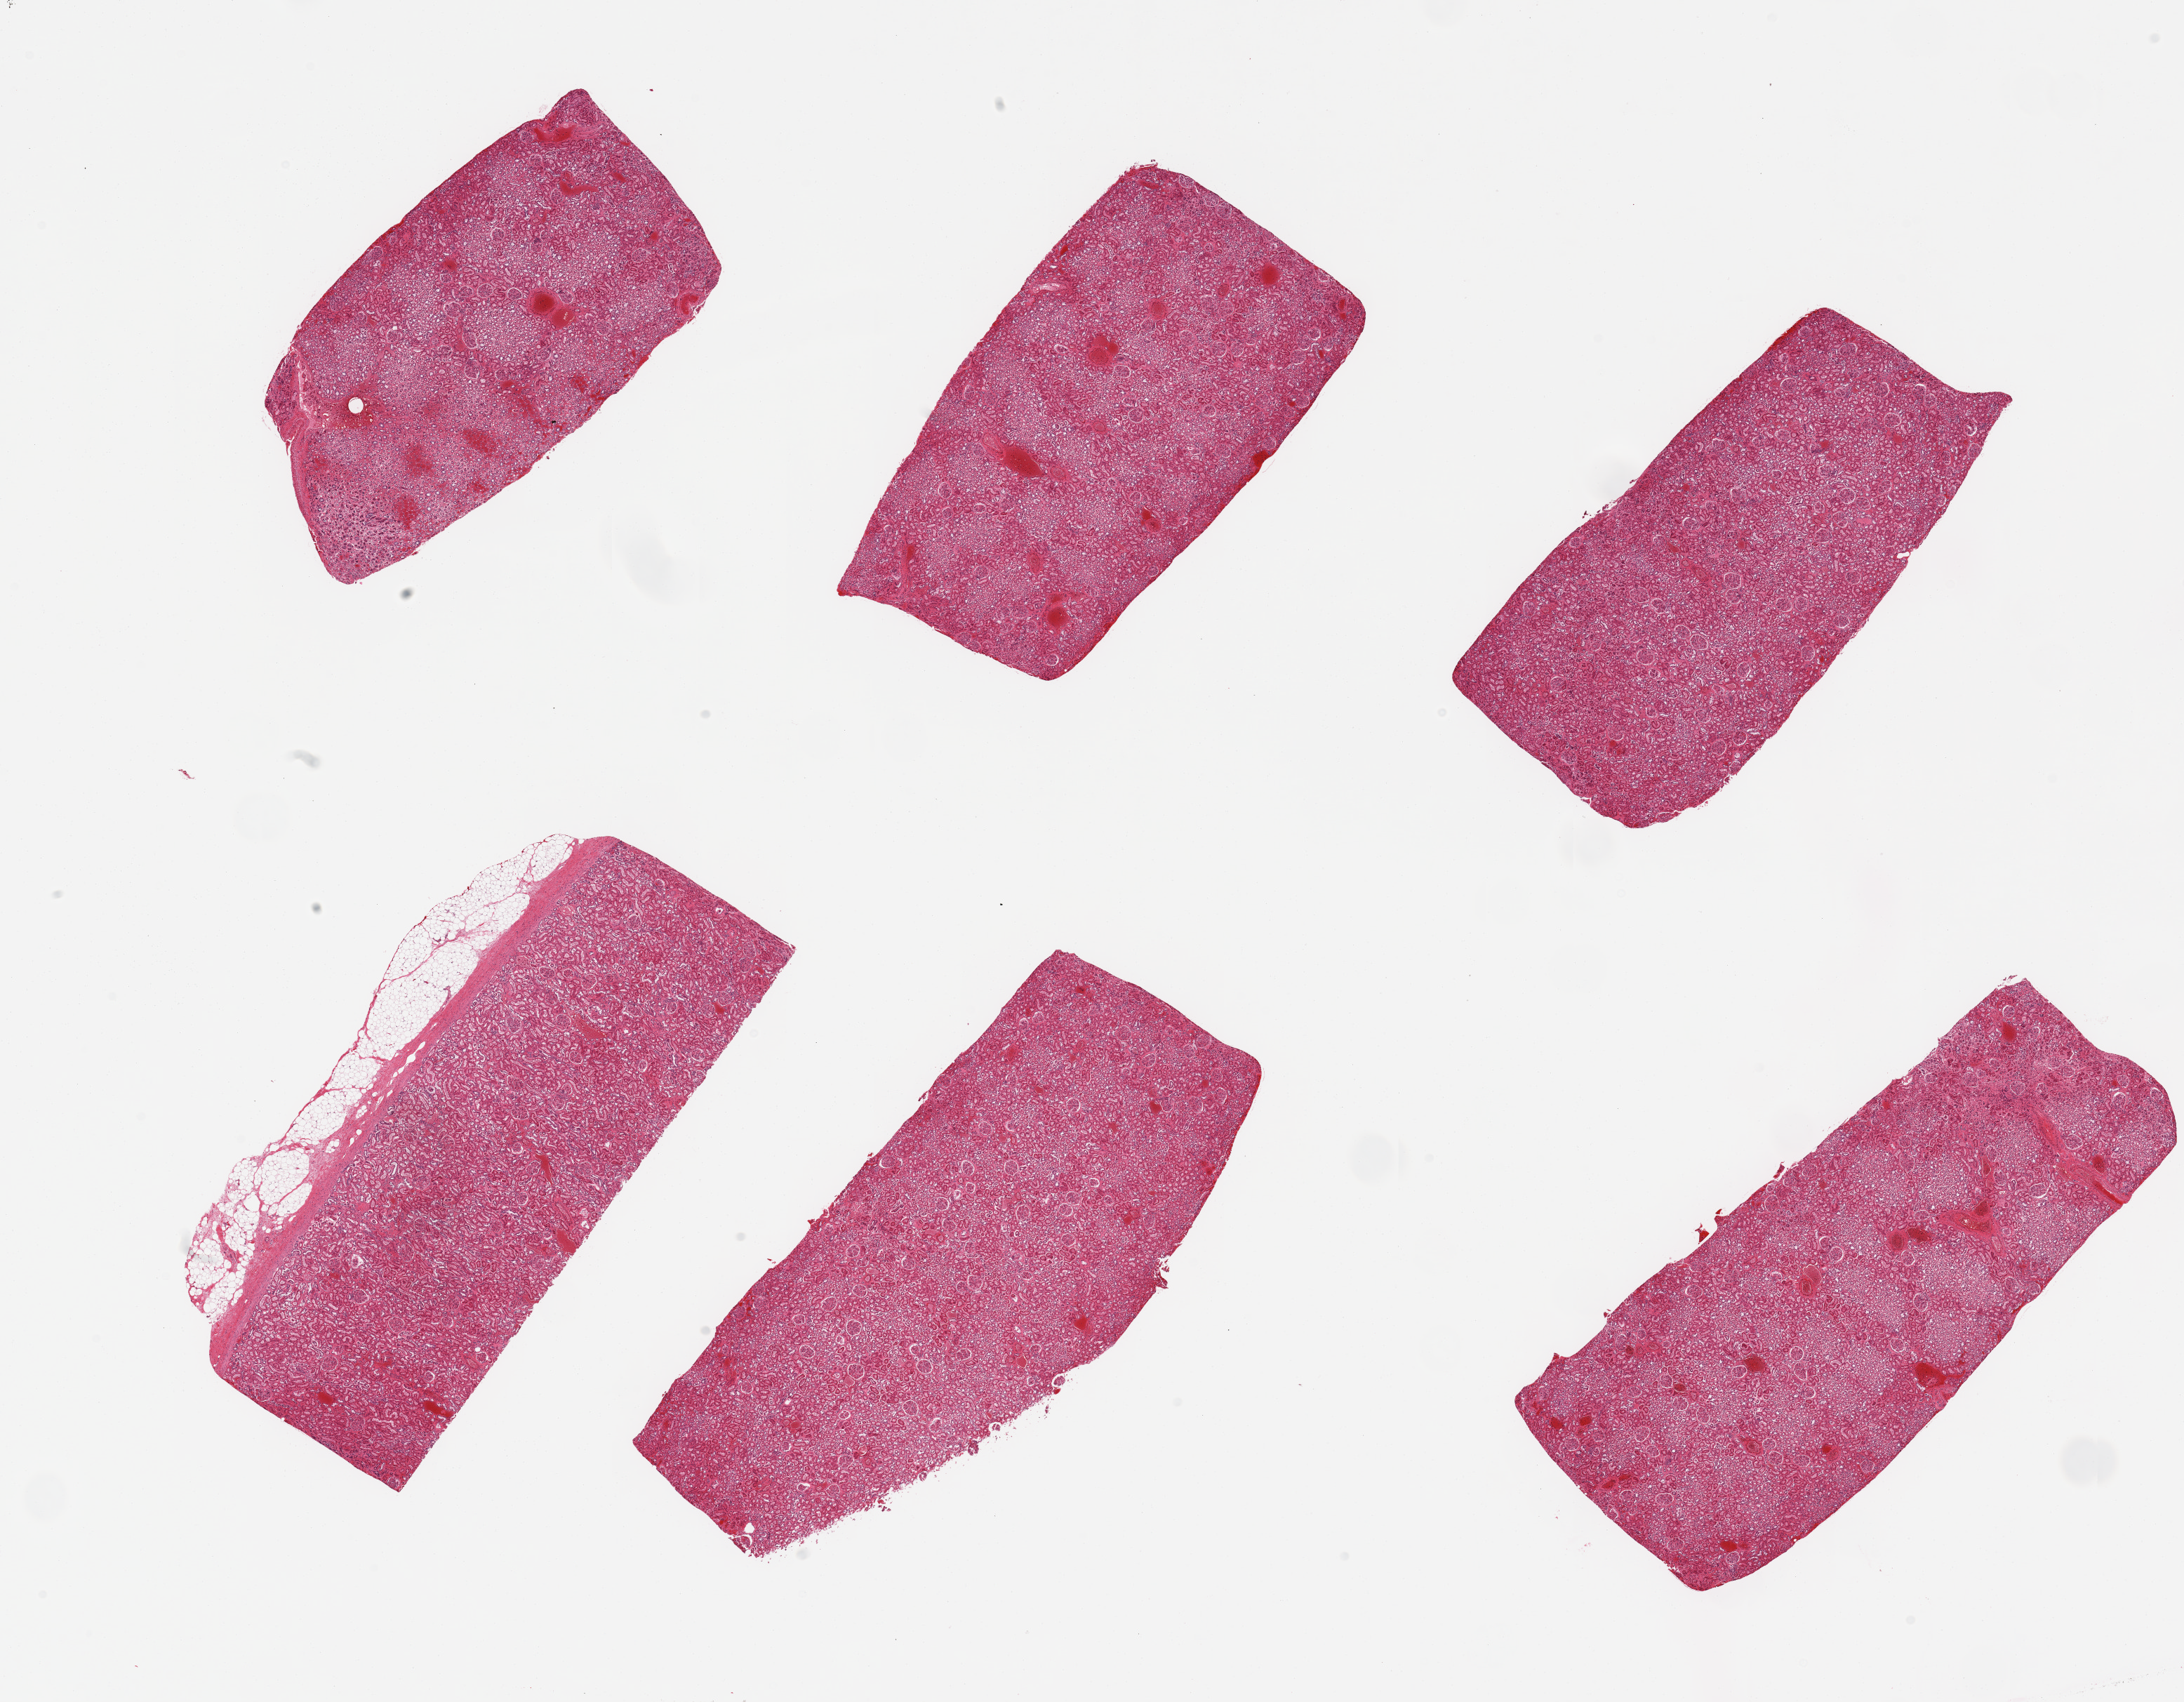
Digitized haematoxylin and eosin-stained section, whole scanned area (about 24.6 x 19.2 mm) shown as a low-resolution overview. PAXgene-fixed paraffin-embedded (PFPE) section. Target tissue: renal cortex. Tissue donor sample. Donor: male.
Review note (as recorded): 6 pieces; glomeruli in all sections, congestion, 1 piece has ~15% attached fat.